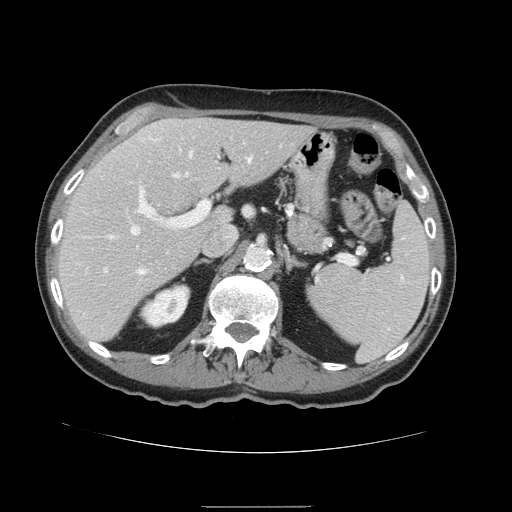
Contrast-enhanced abdominal CT, one axial slice. Position 95 of 168 along the scan axis. Intravenous contrast given. Soft-tissue window (W 400 / L 40 HU). 2.5 mm slice thickness. 512 × 512 image matrix, field of view 386 × 386 mm. Male patient, age 74 years. Case-level facts recorded for this patient, not image findings: diagnosis: colorectal cancer liver metastases, imaged before liver resection; multiple liver metastases: no; largest metastasis: 14.5 cm; chemotherapy before resection: no.
Annotated regions visible in this slice (outlined manually by an expert reader):
- hepatic veins: box from (x=131, y=153) to (x=252, y=273) px
- liver: (x=58, y=119)–(x=316, y=343)
- planned liver remnant (the part of the liver to remain after resection): (x=58, y=119)–(x=316, y=343)
- portal vein (with intrahepatic branches): (x=84, y=188)–(x=210, y=271)